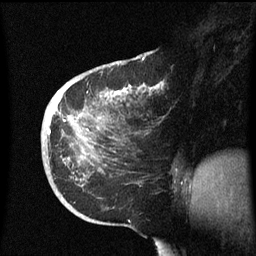
Breast MRI (dynamic contrast-enhanced), one sagittal slice. Position 24 of 60 along the scan axis. Dynamic contrast-enhanced series, image 2 of 3 at this slice position (ordered by acquisition). 1.5 T. TE 4.2 ms, TR 8.4 ms. 2.3 mm slice thickness. 256 × 256 image matrix, field of view 200 × 200 mm. Patient: female, 38 years. Case-level facts recorded for this patient, not image findings: setting: breast cancer imaged before/during neoadjuvant chemotherapy; receptor status: HER2-positive.
Annotated regions visible in this slice (semi-automatically segmented with operator editing):
- analysis volume of interest (the breast-tissue region the enhancement analysis was run in; not a lesion): bounding box [x1, y1, x2, y2] px = [41, 78, 162, 213]
- tumour enhancement mask (voxels above the 70 % enhancement threshold inside the analysis volume of interest): [48, 84, 160, 133]